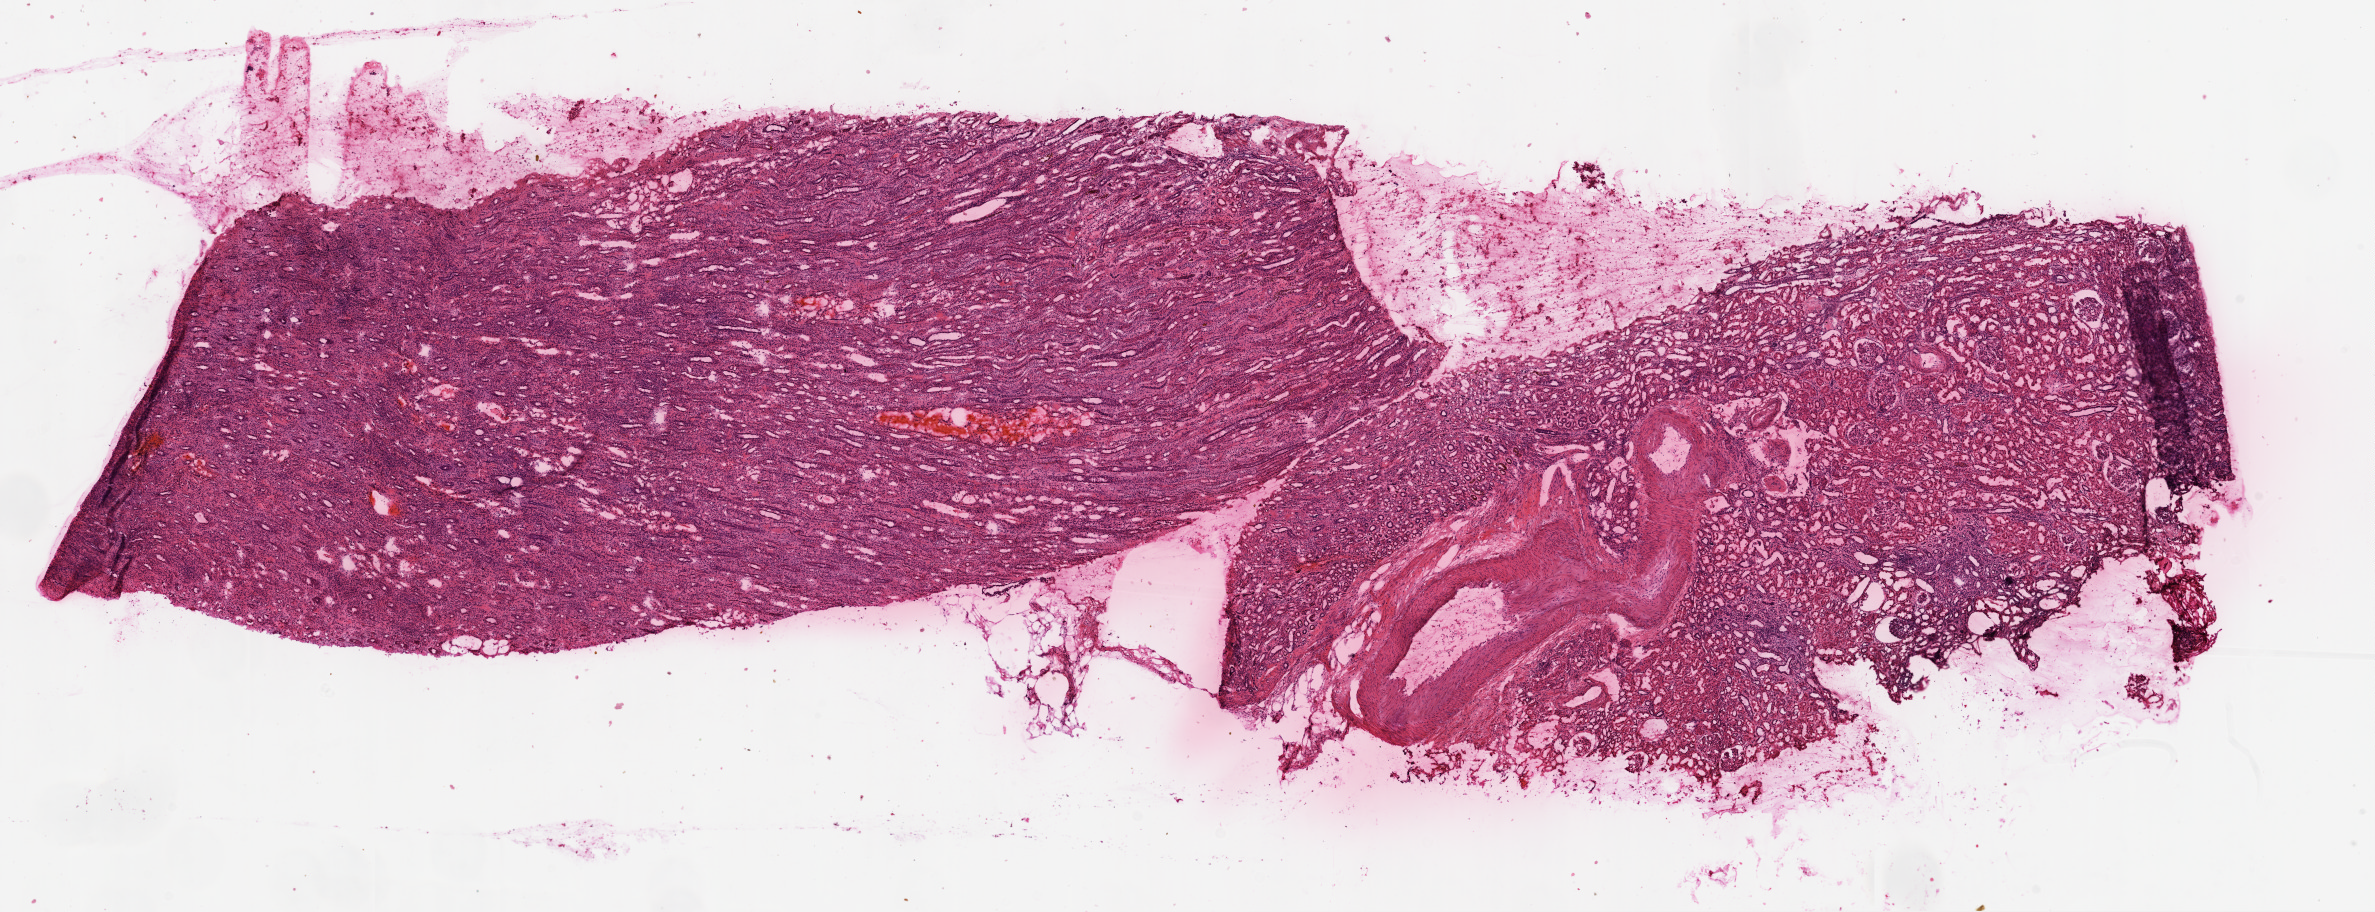
Hematoxylin and eosin (H&E) stained whole-slide image, a low-resolution overview of the entire scanned area, about 19.1 x 7.3 mm (slide scanned at 20x); frozen section from the top of the tissue portion; solid tissue normal (non-tumour tissue) sample from the kidney. Female, age 64 years at initial diagnosis.
* this section: solid tissue normal (non-tumour) sample from the same patient
* patient diagnosis: Clear cell adenocarcinoma, NOS